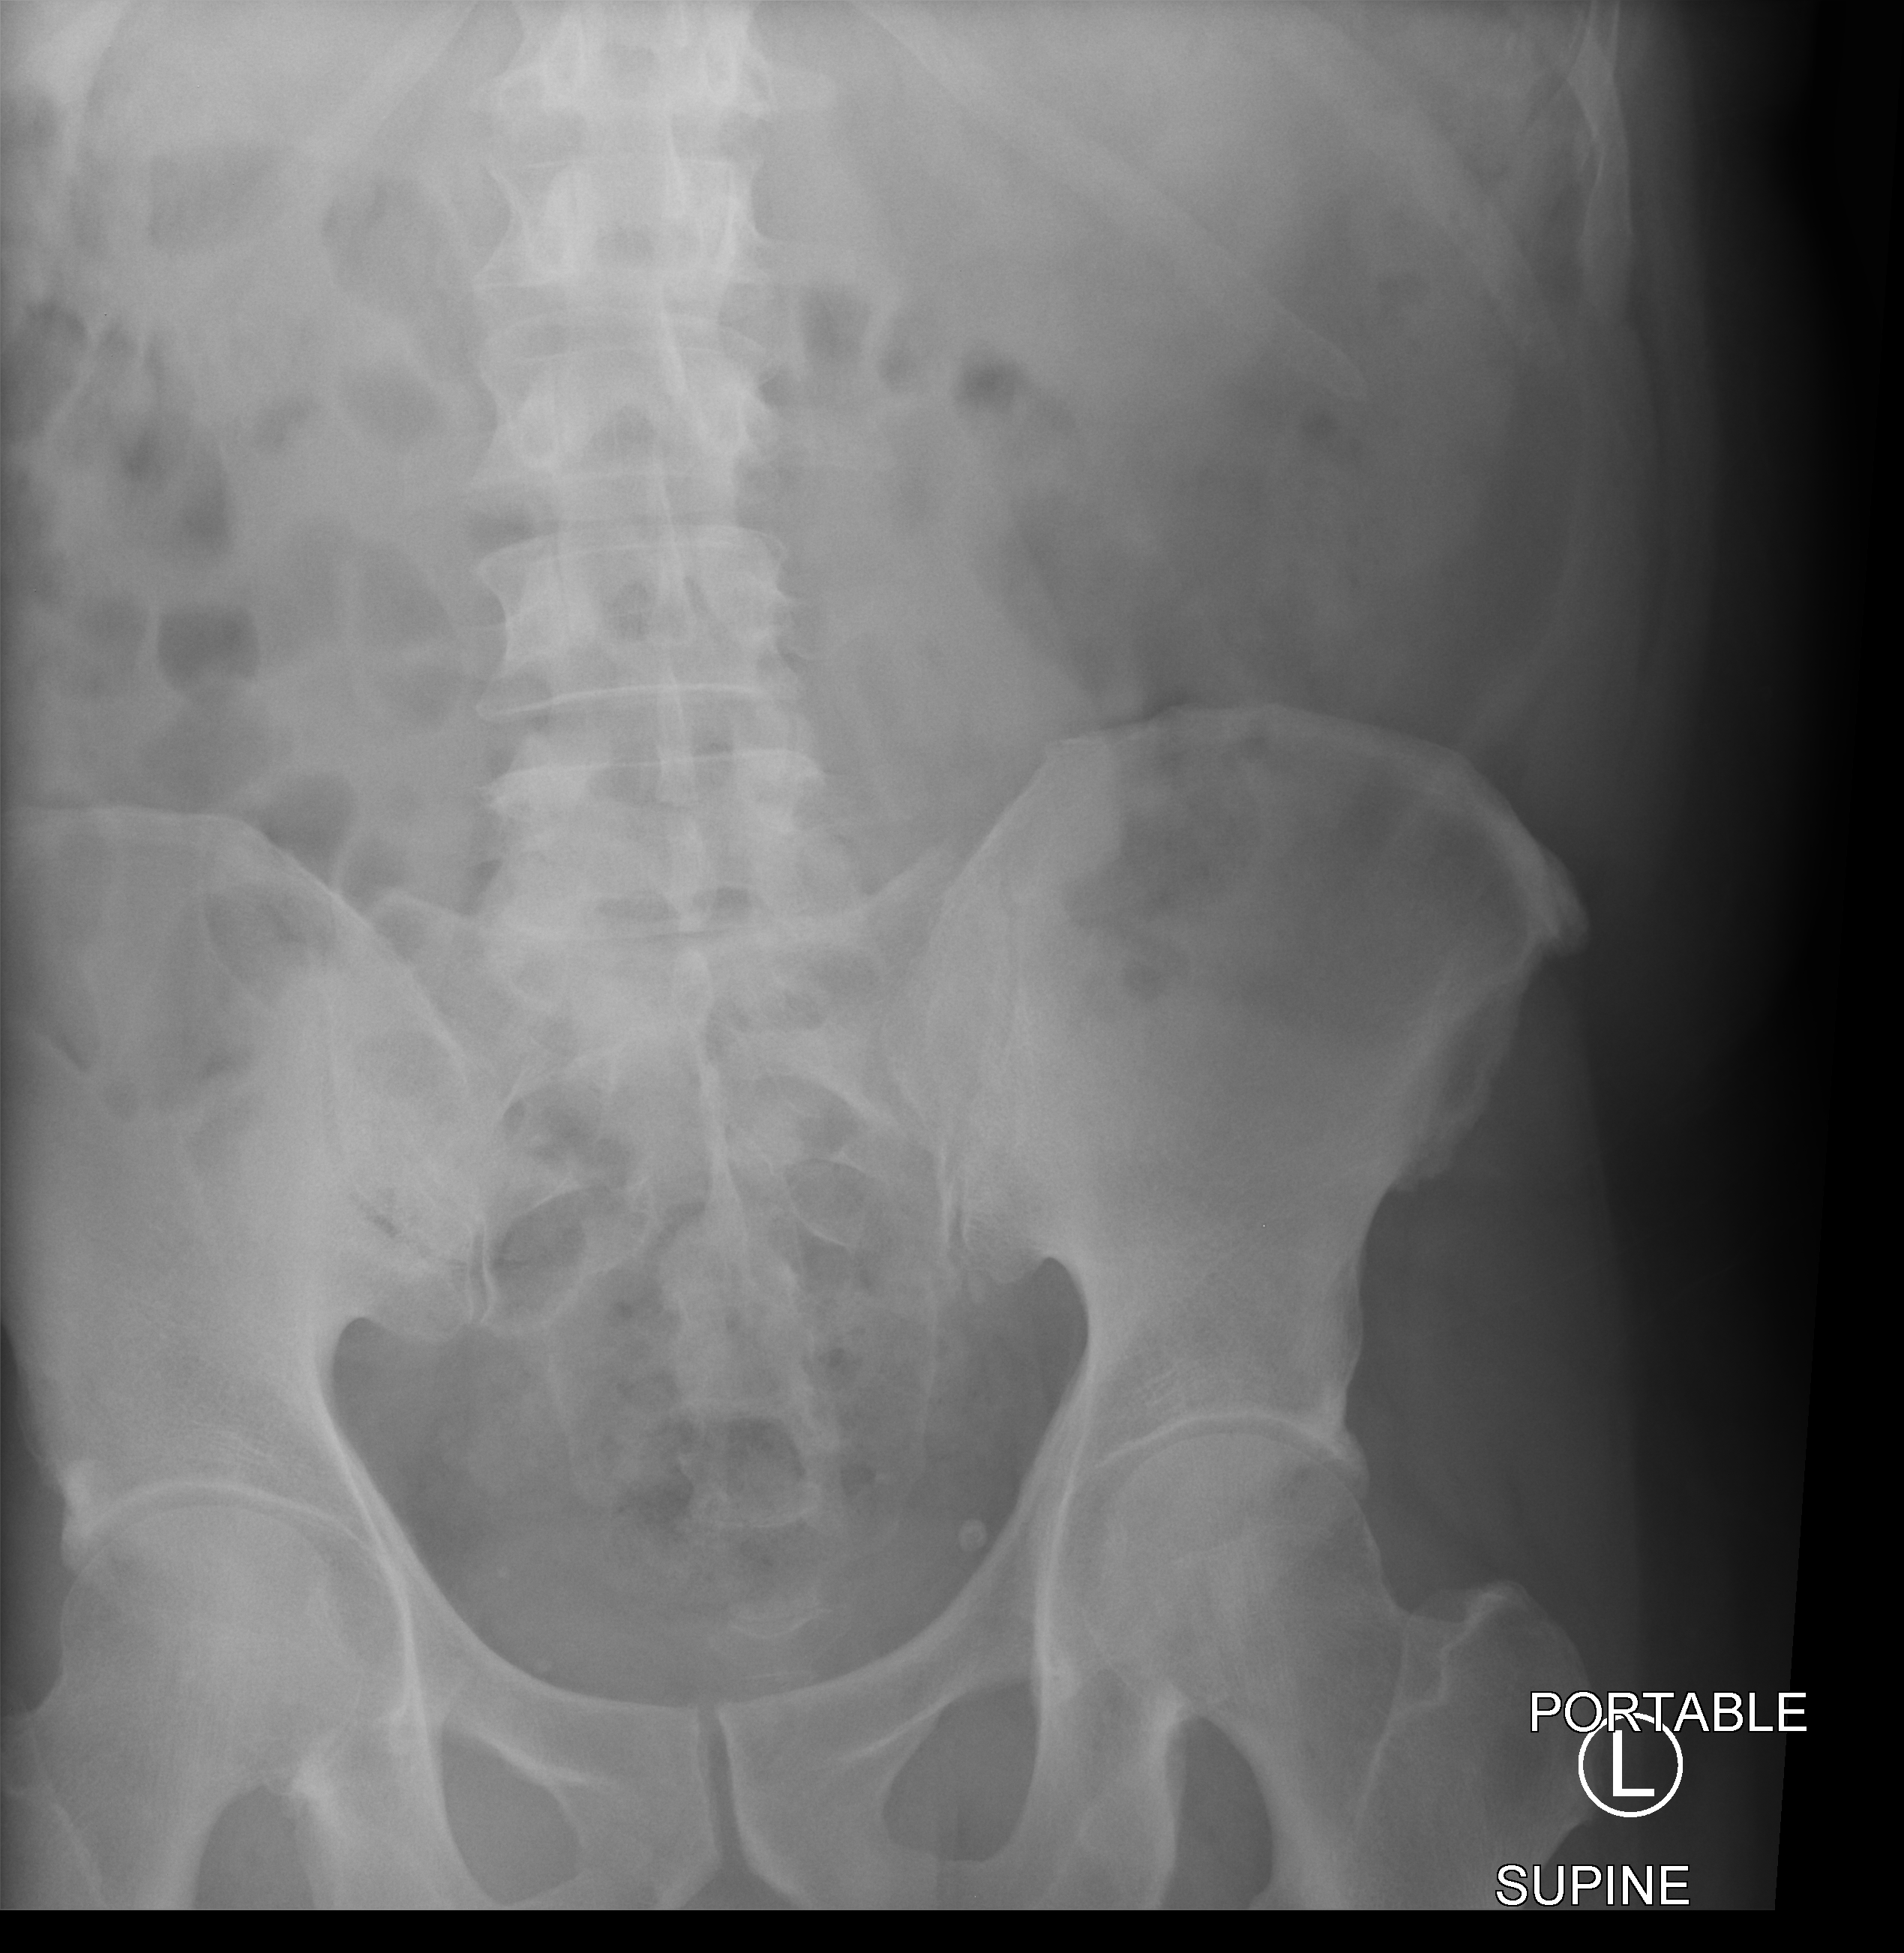
Bedside abdomen radiograph (computed radiography); anteroposterior (AP) projection. Male patient hospitalised with COVID-19, age 18–59 years.
From the hospital-stay record, not from the radiograph (when in the stay this image was taken is not recorded): admitted to intensive care during this hospital stay: yes; COPD (admission record): no; mechanically ventilated during this hospital stay: no.